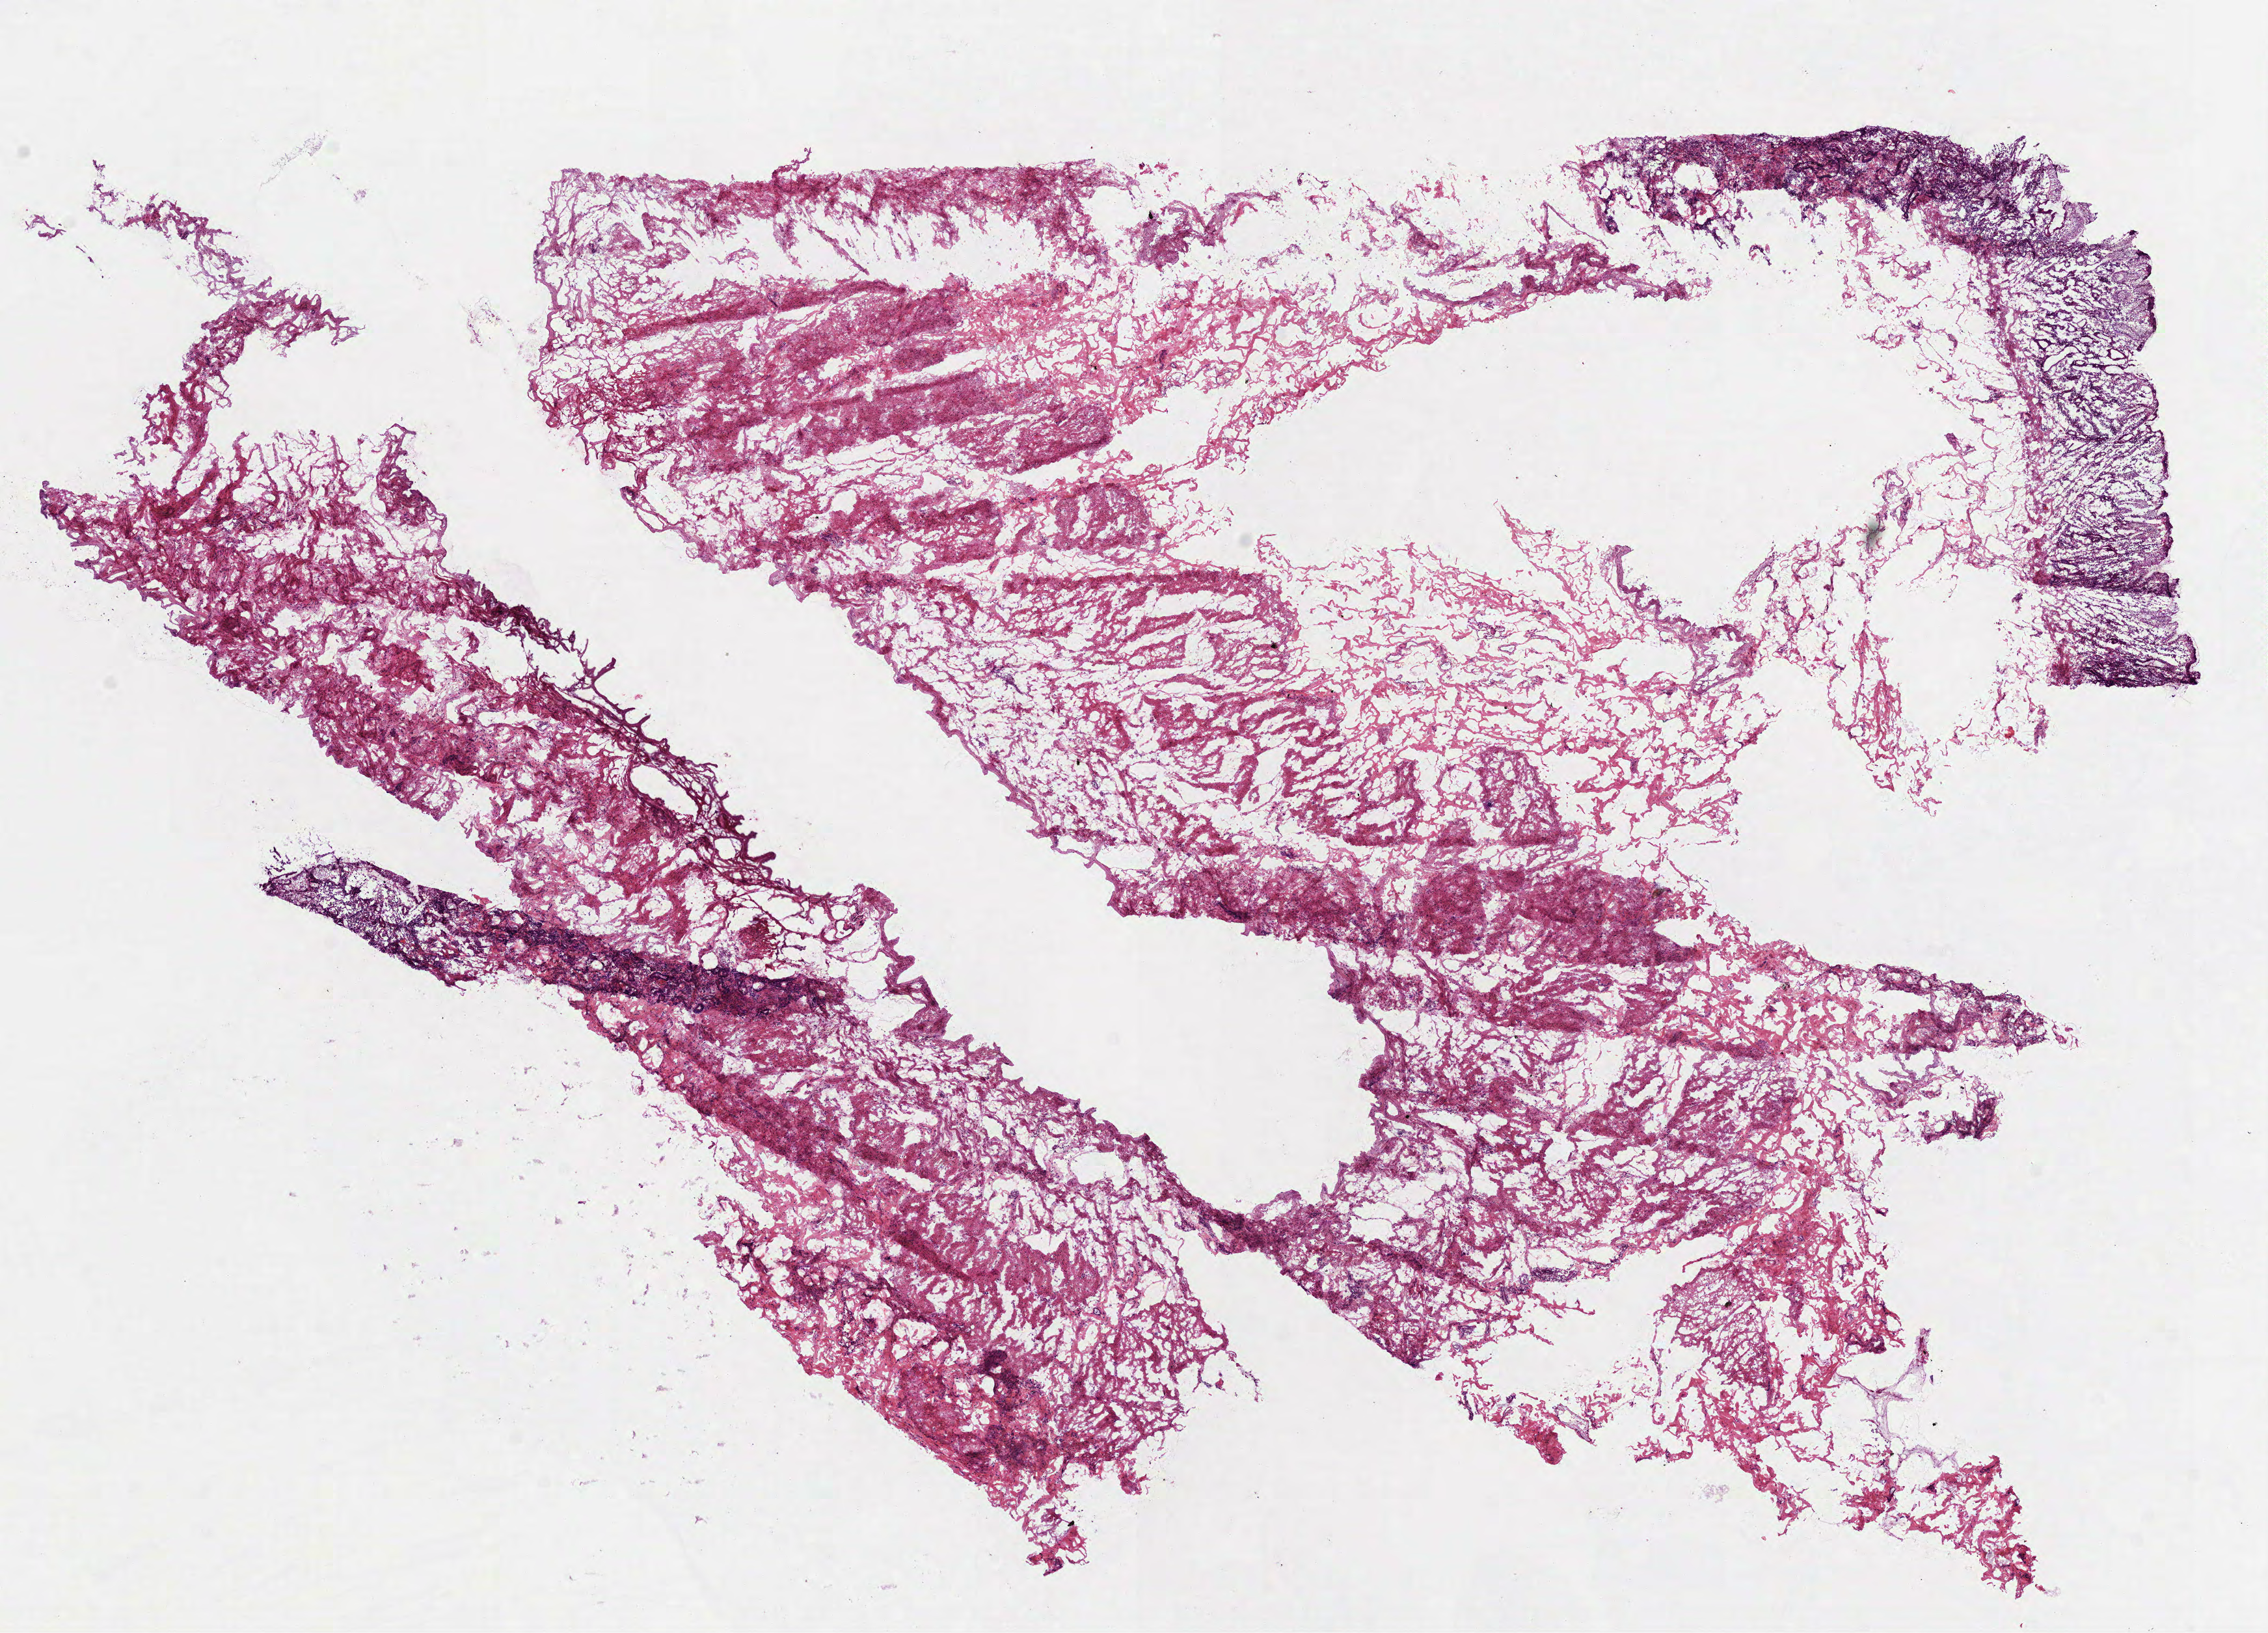
Digitized H&E-stained tissue section (whole slide) — a low-resolution overview of the entire scanned area, about 14.1 x 10.1 mm (slide scanned at 40x); frozen section from the top of the tissue portion; sample: solid tissue normal (non-tumour tissue), stomach. Female, age 74 years at initial diagnosis.
* this section: solid tissue normal (non-tumour) sample from the same patient
* patient diagnosis: Adenocarcinoma, NOS (body of stomach)